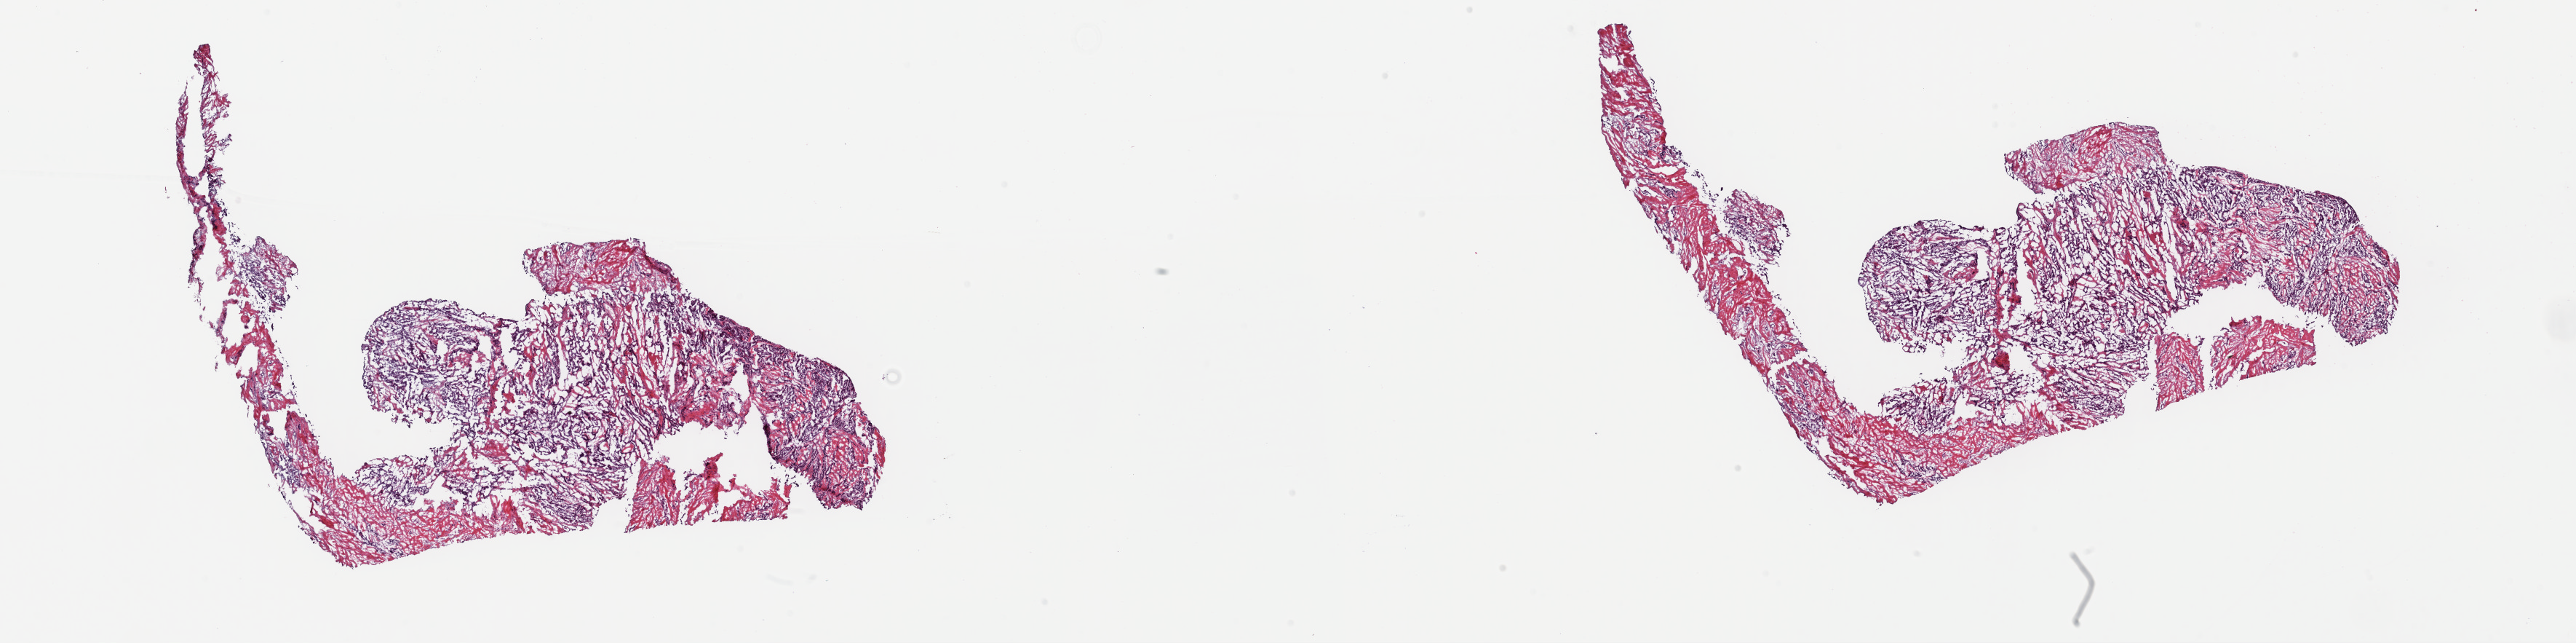
Hematoxylin and eosin (H&E) stained whole-slide image — a low-resolution overview of the entire scanned area, about 28.0 x 7.0 mm (from a 40x scan); frozen section from the top of the tissue portion; thyroid, primary tumour sample. Male, age 66 years at initial diagnosis. Slide review estimates, as recorded: tumour cells 50%, tumour nuclei 100%, normal cells 0%, stromal cells 50%, necrosis 0%. Inflammatory infiltration, as recorded: lymphocyte infiltration 0%, monocyte infiltration 1%, neutrophil infiltration 0%.
AJCC pathologic stage: III (5th edition). Lymph nodes positive (case pathology): 1 of 2 examined. Histologic diagnosis: Papillary adenocarcinoma, NOS (thyroid gland).